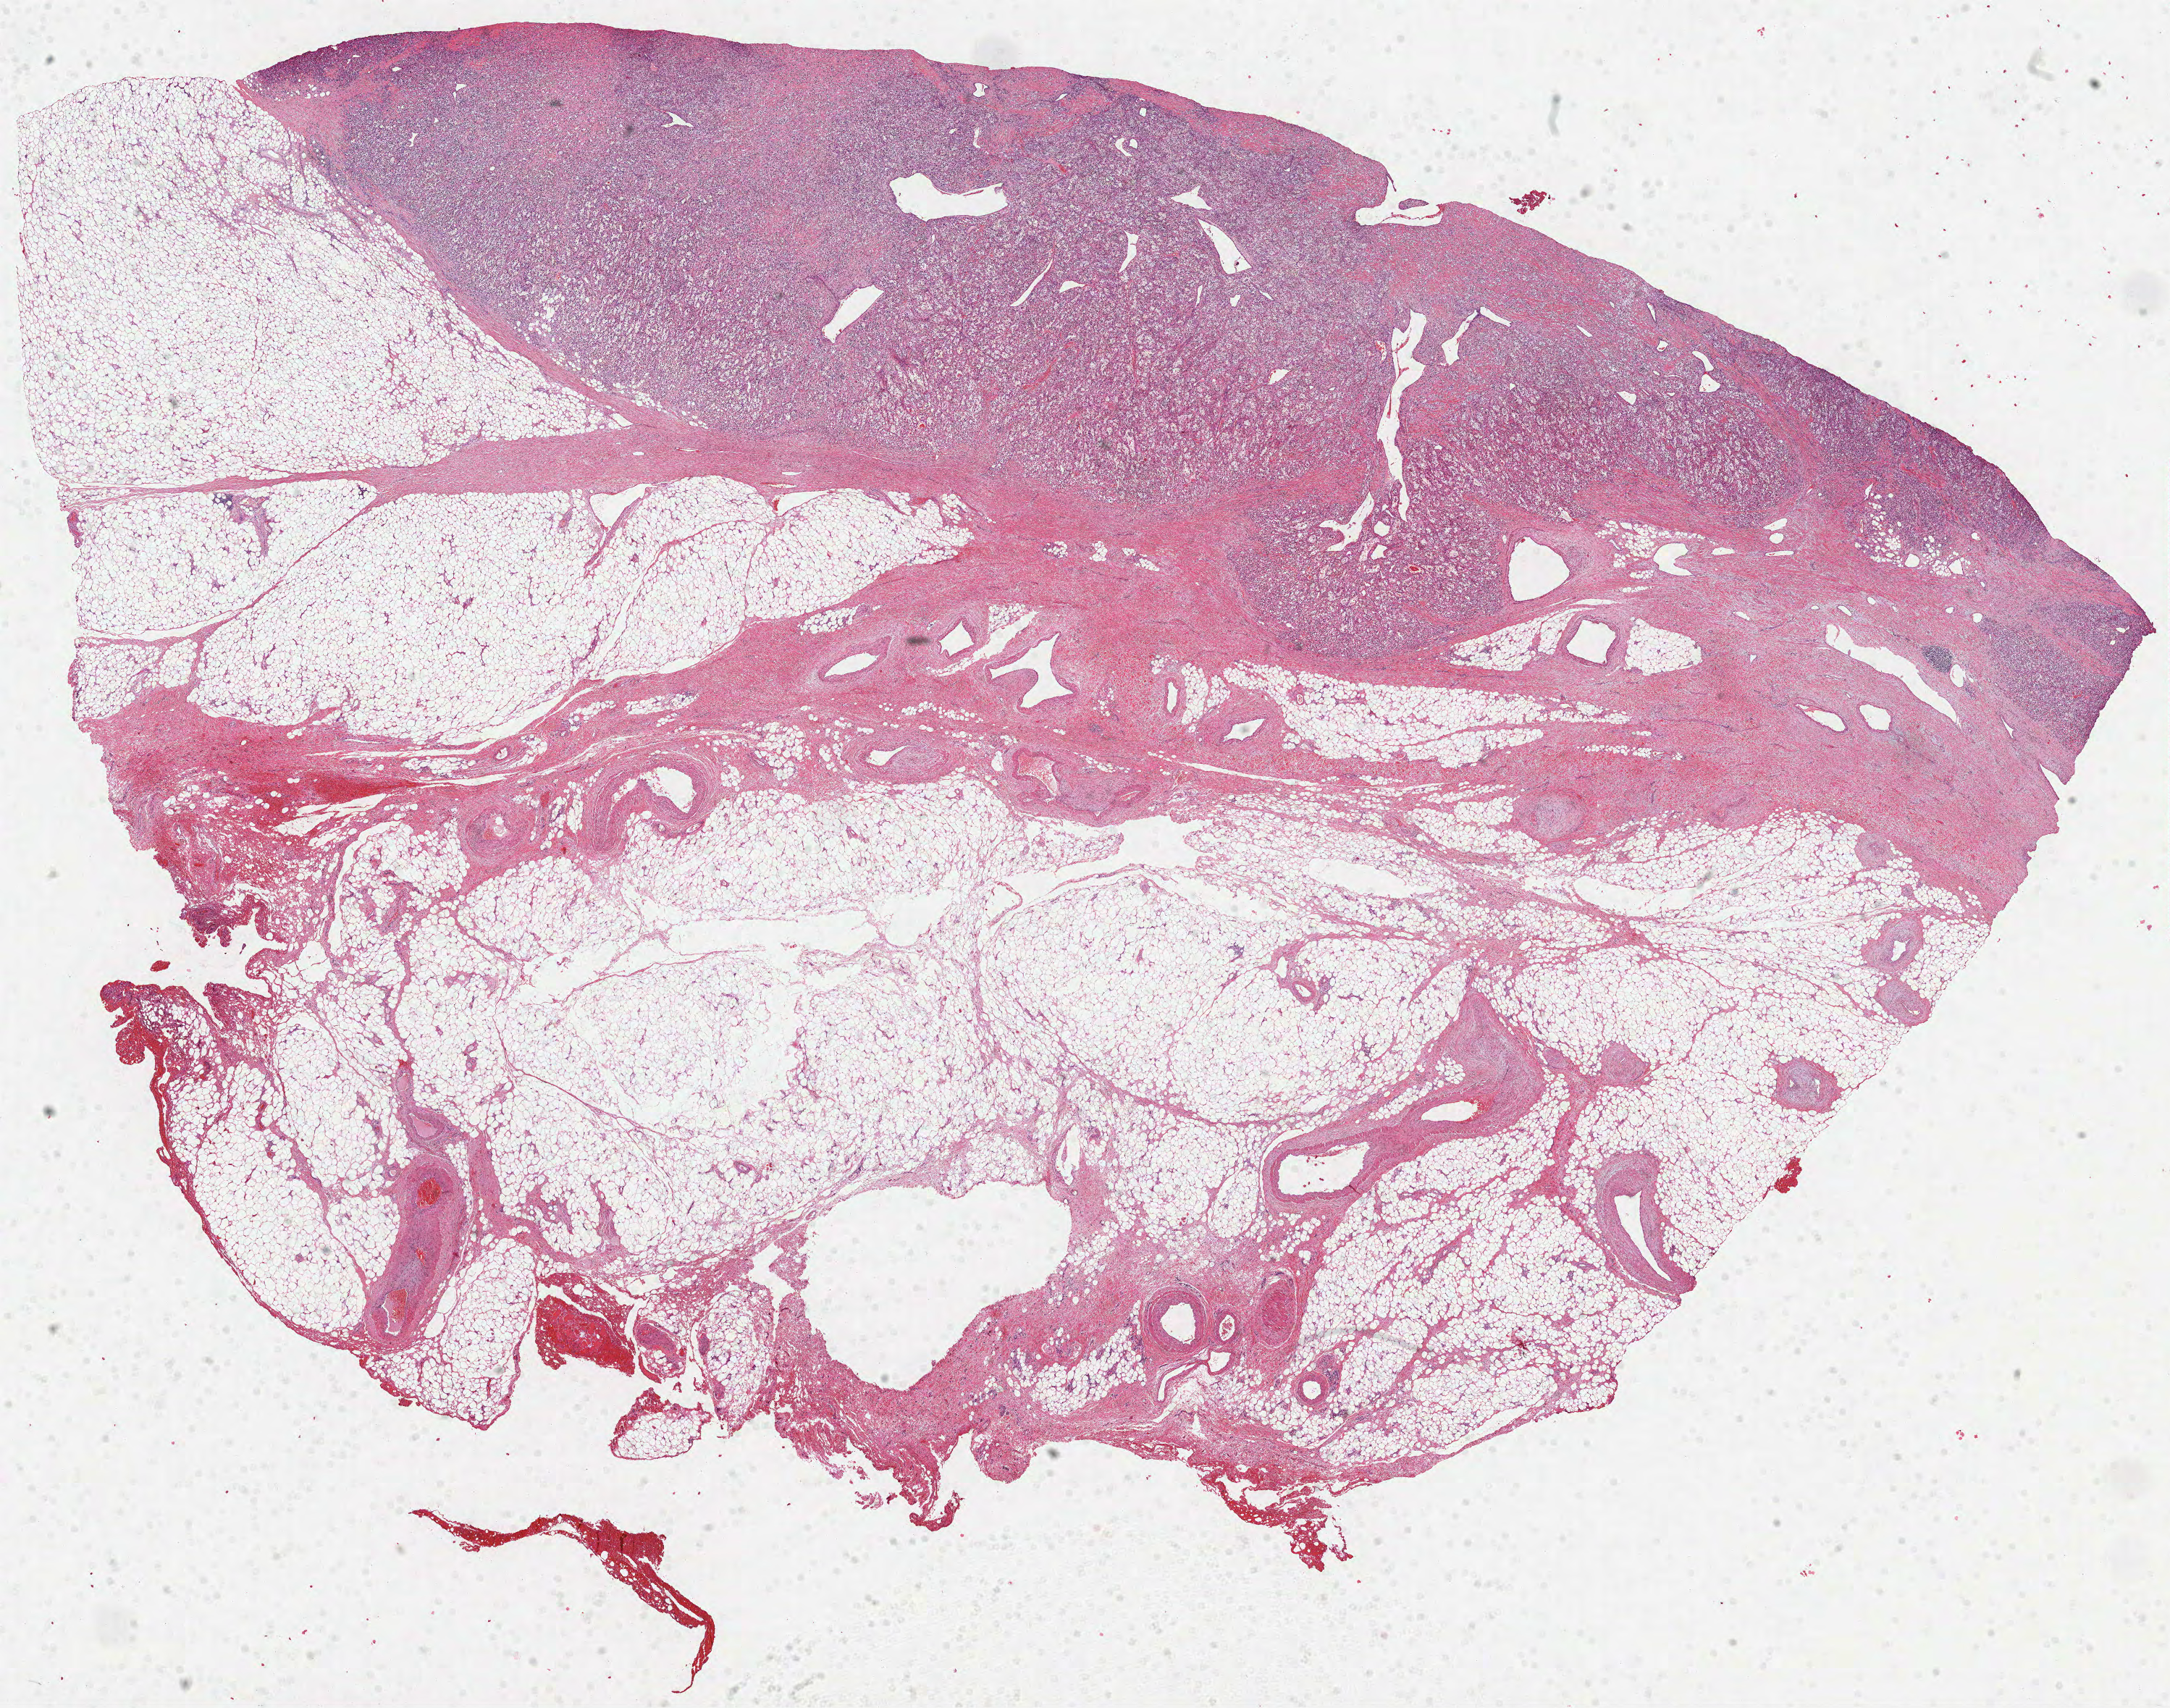
Digitized H&E-stained tissue section (whole slide) — low-resolution overview of the scanned area, about 24.2 x 19.0 mm, formalin-fixed paraffin-embedded (FFPE) diagnostic section, primary tumour sample from the kidney. Patient: male, age at initial diagnosis 64 years. Histologic grade: G4 (undifferentiated).
* AJCC pathologic stage: IV (7th edition)
* laterality: left
* diagnosis: Clear cell adenocarcinoma, NOS